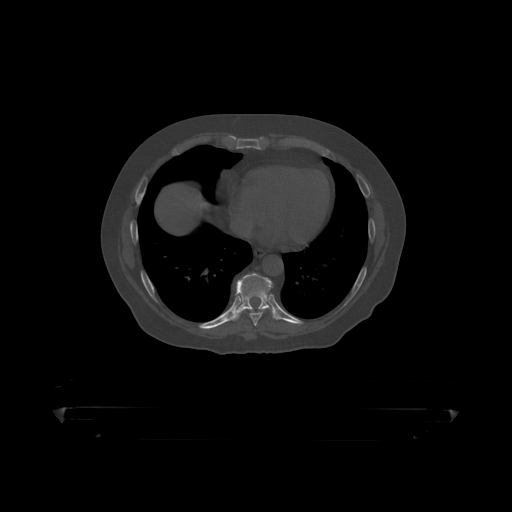
CT including the spine, one axial slice. Position 246 of 390 along the scan axis. Bone window (W 1800 / L 400 HU). 1.25 mm slice thickness. 512 × 512 image matrix, field of view 650 × 650 mm. Male patient, age 60 years. From the clinical record (not read from this slice): primary cancer: prostate.
Annotated regions visible in this slice (semi-automatically segmented with operator editing):
- T8 vertebra: bounding box (x1, y1, x2, y2) in pixels: (250, 284, 274, 319)
- T9 vertebra: (233, 274, 274, 317)